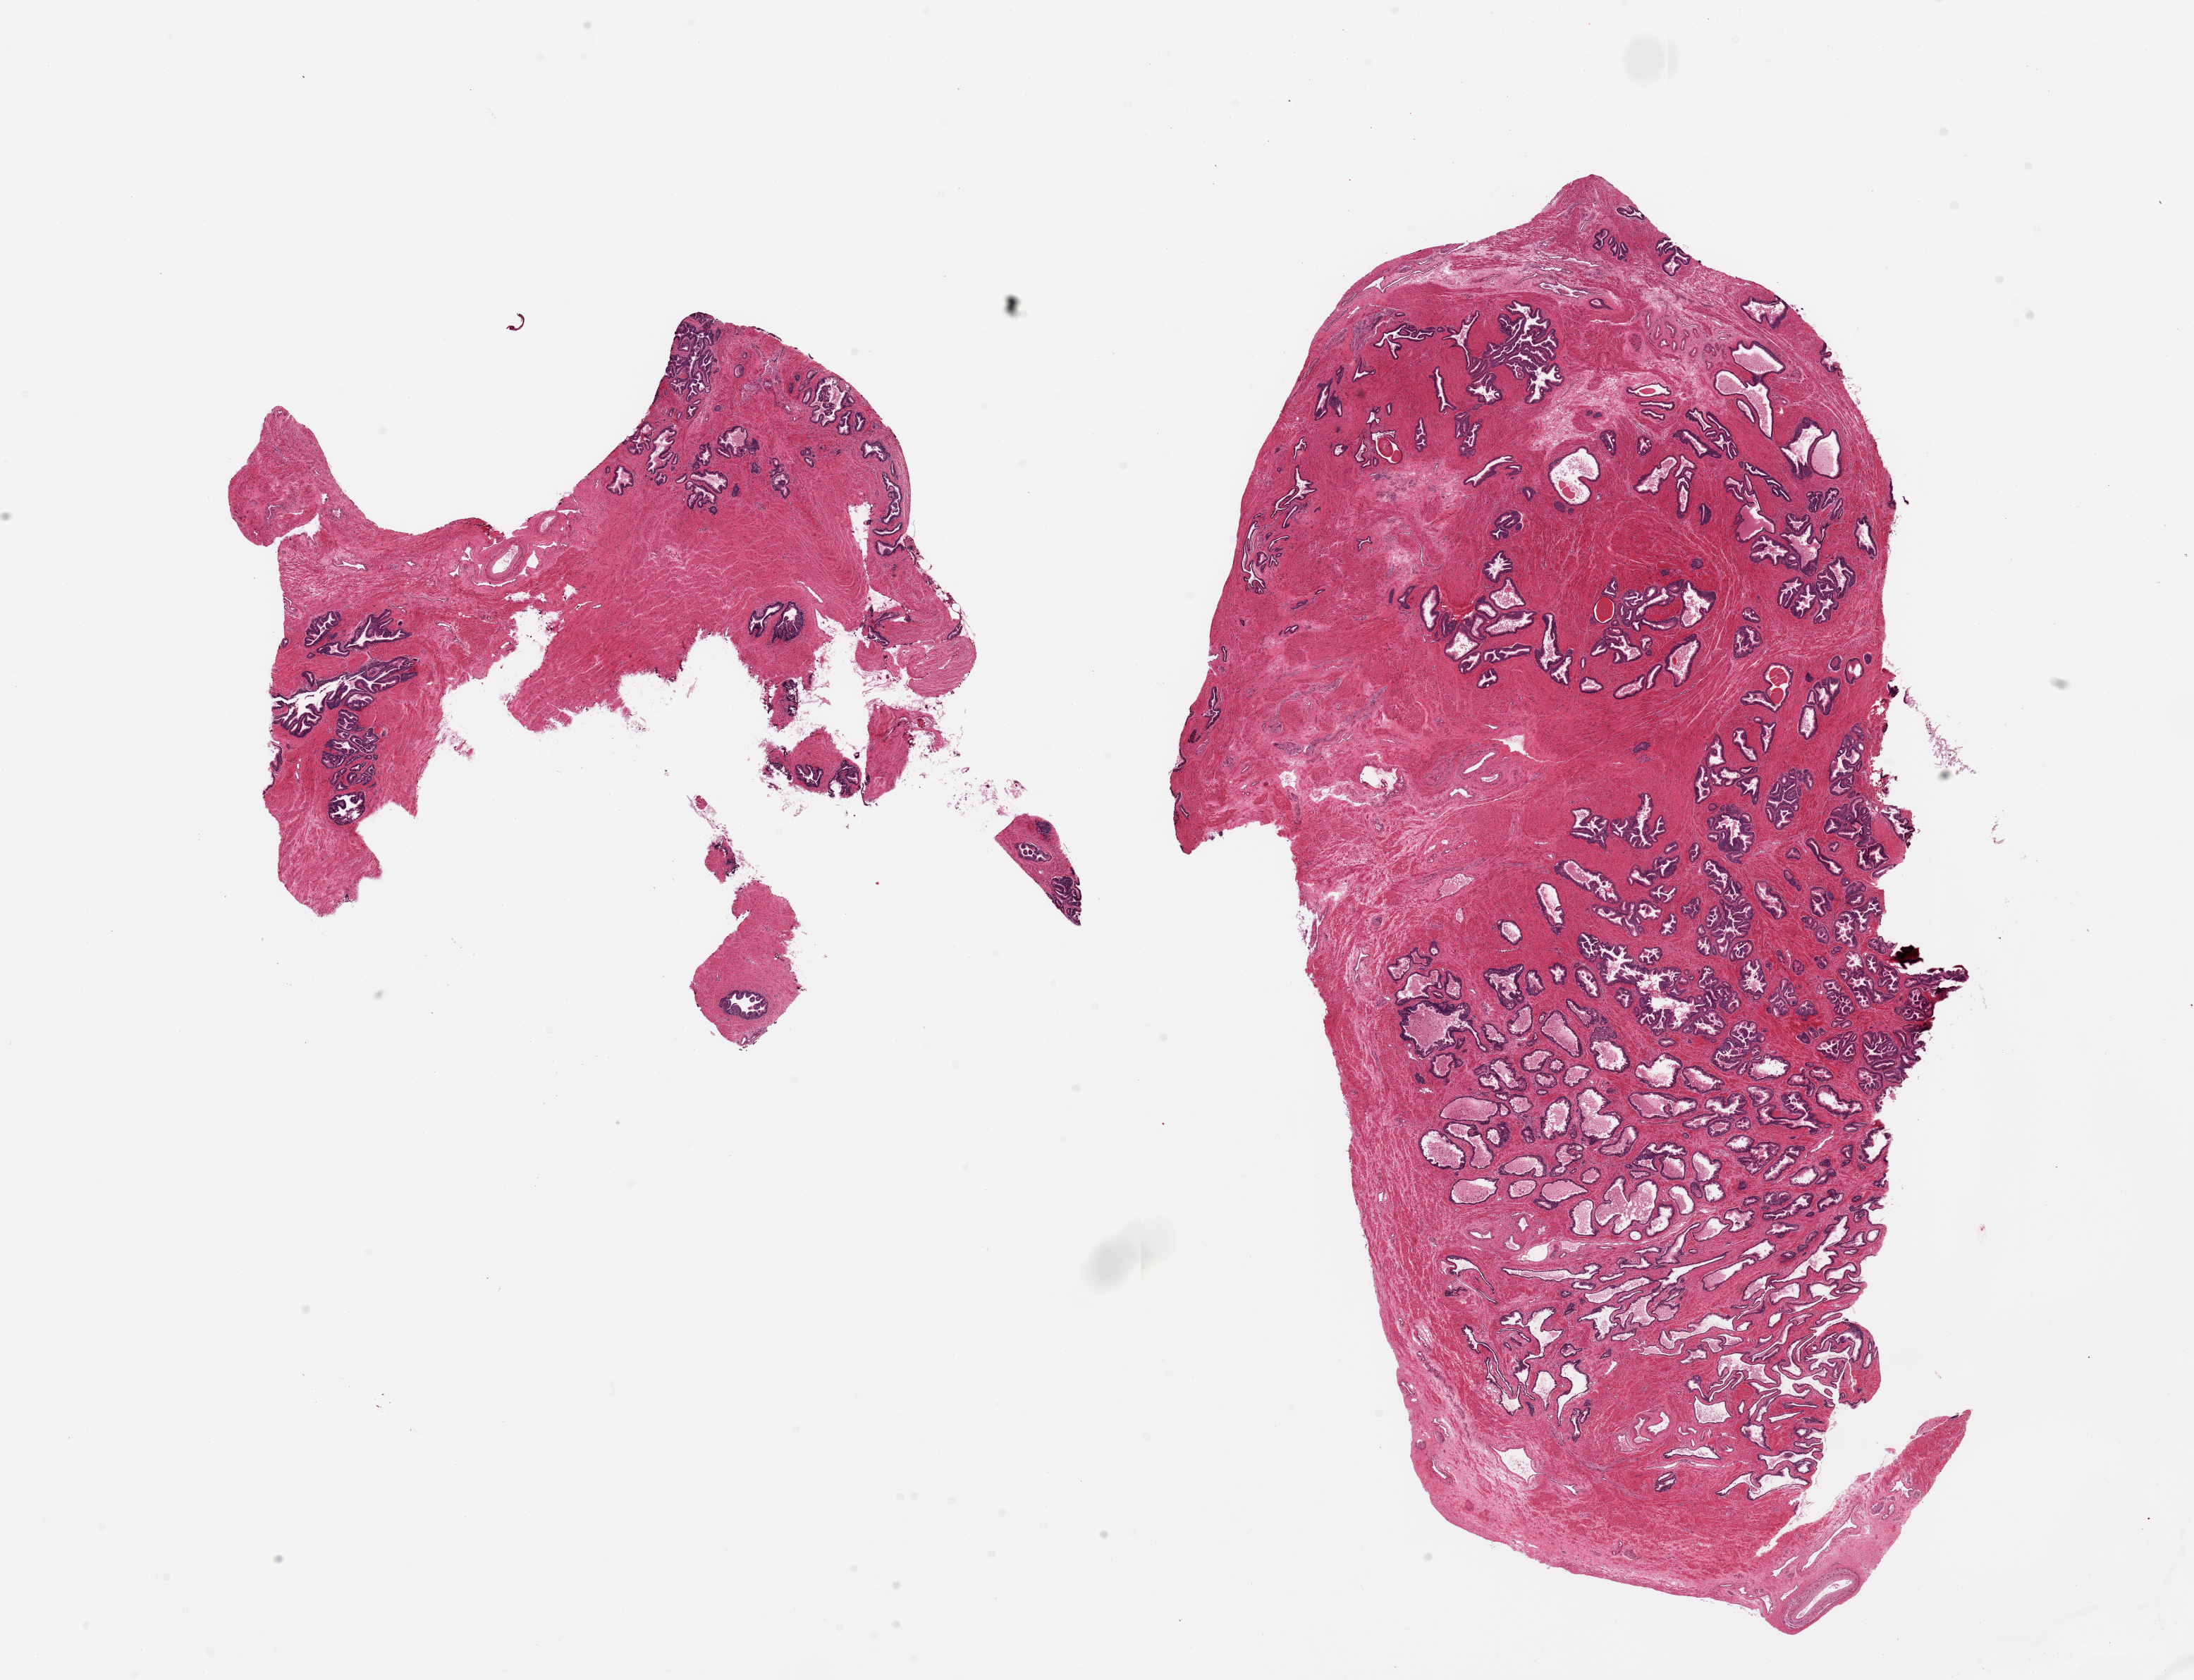
Haematoxylin and eosin whole-slide image — low-resolution overview of the scanned area, about 24.6 x 18.8 mm. PAXgene-fixed paraffin-embedded (PFPE) section. Sampled site (target tissue): prostate. Tissue donor sample. Male donor.
Reviewer comment on this tissue sample: 2 pieces; fibromuscular stroma and glandular component.